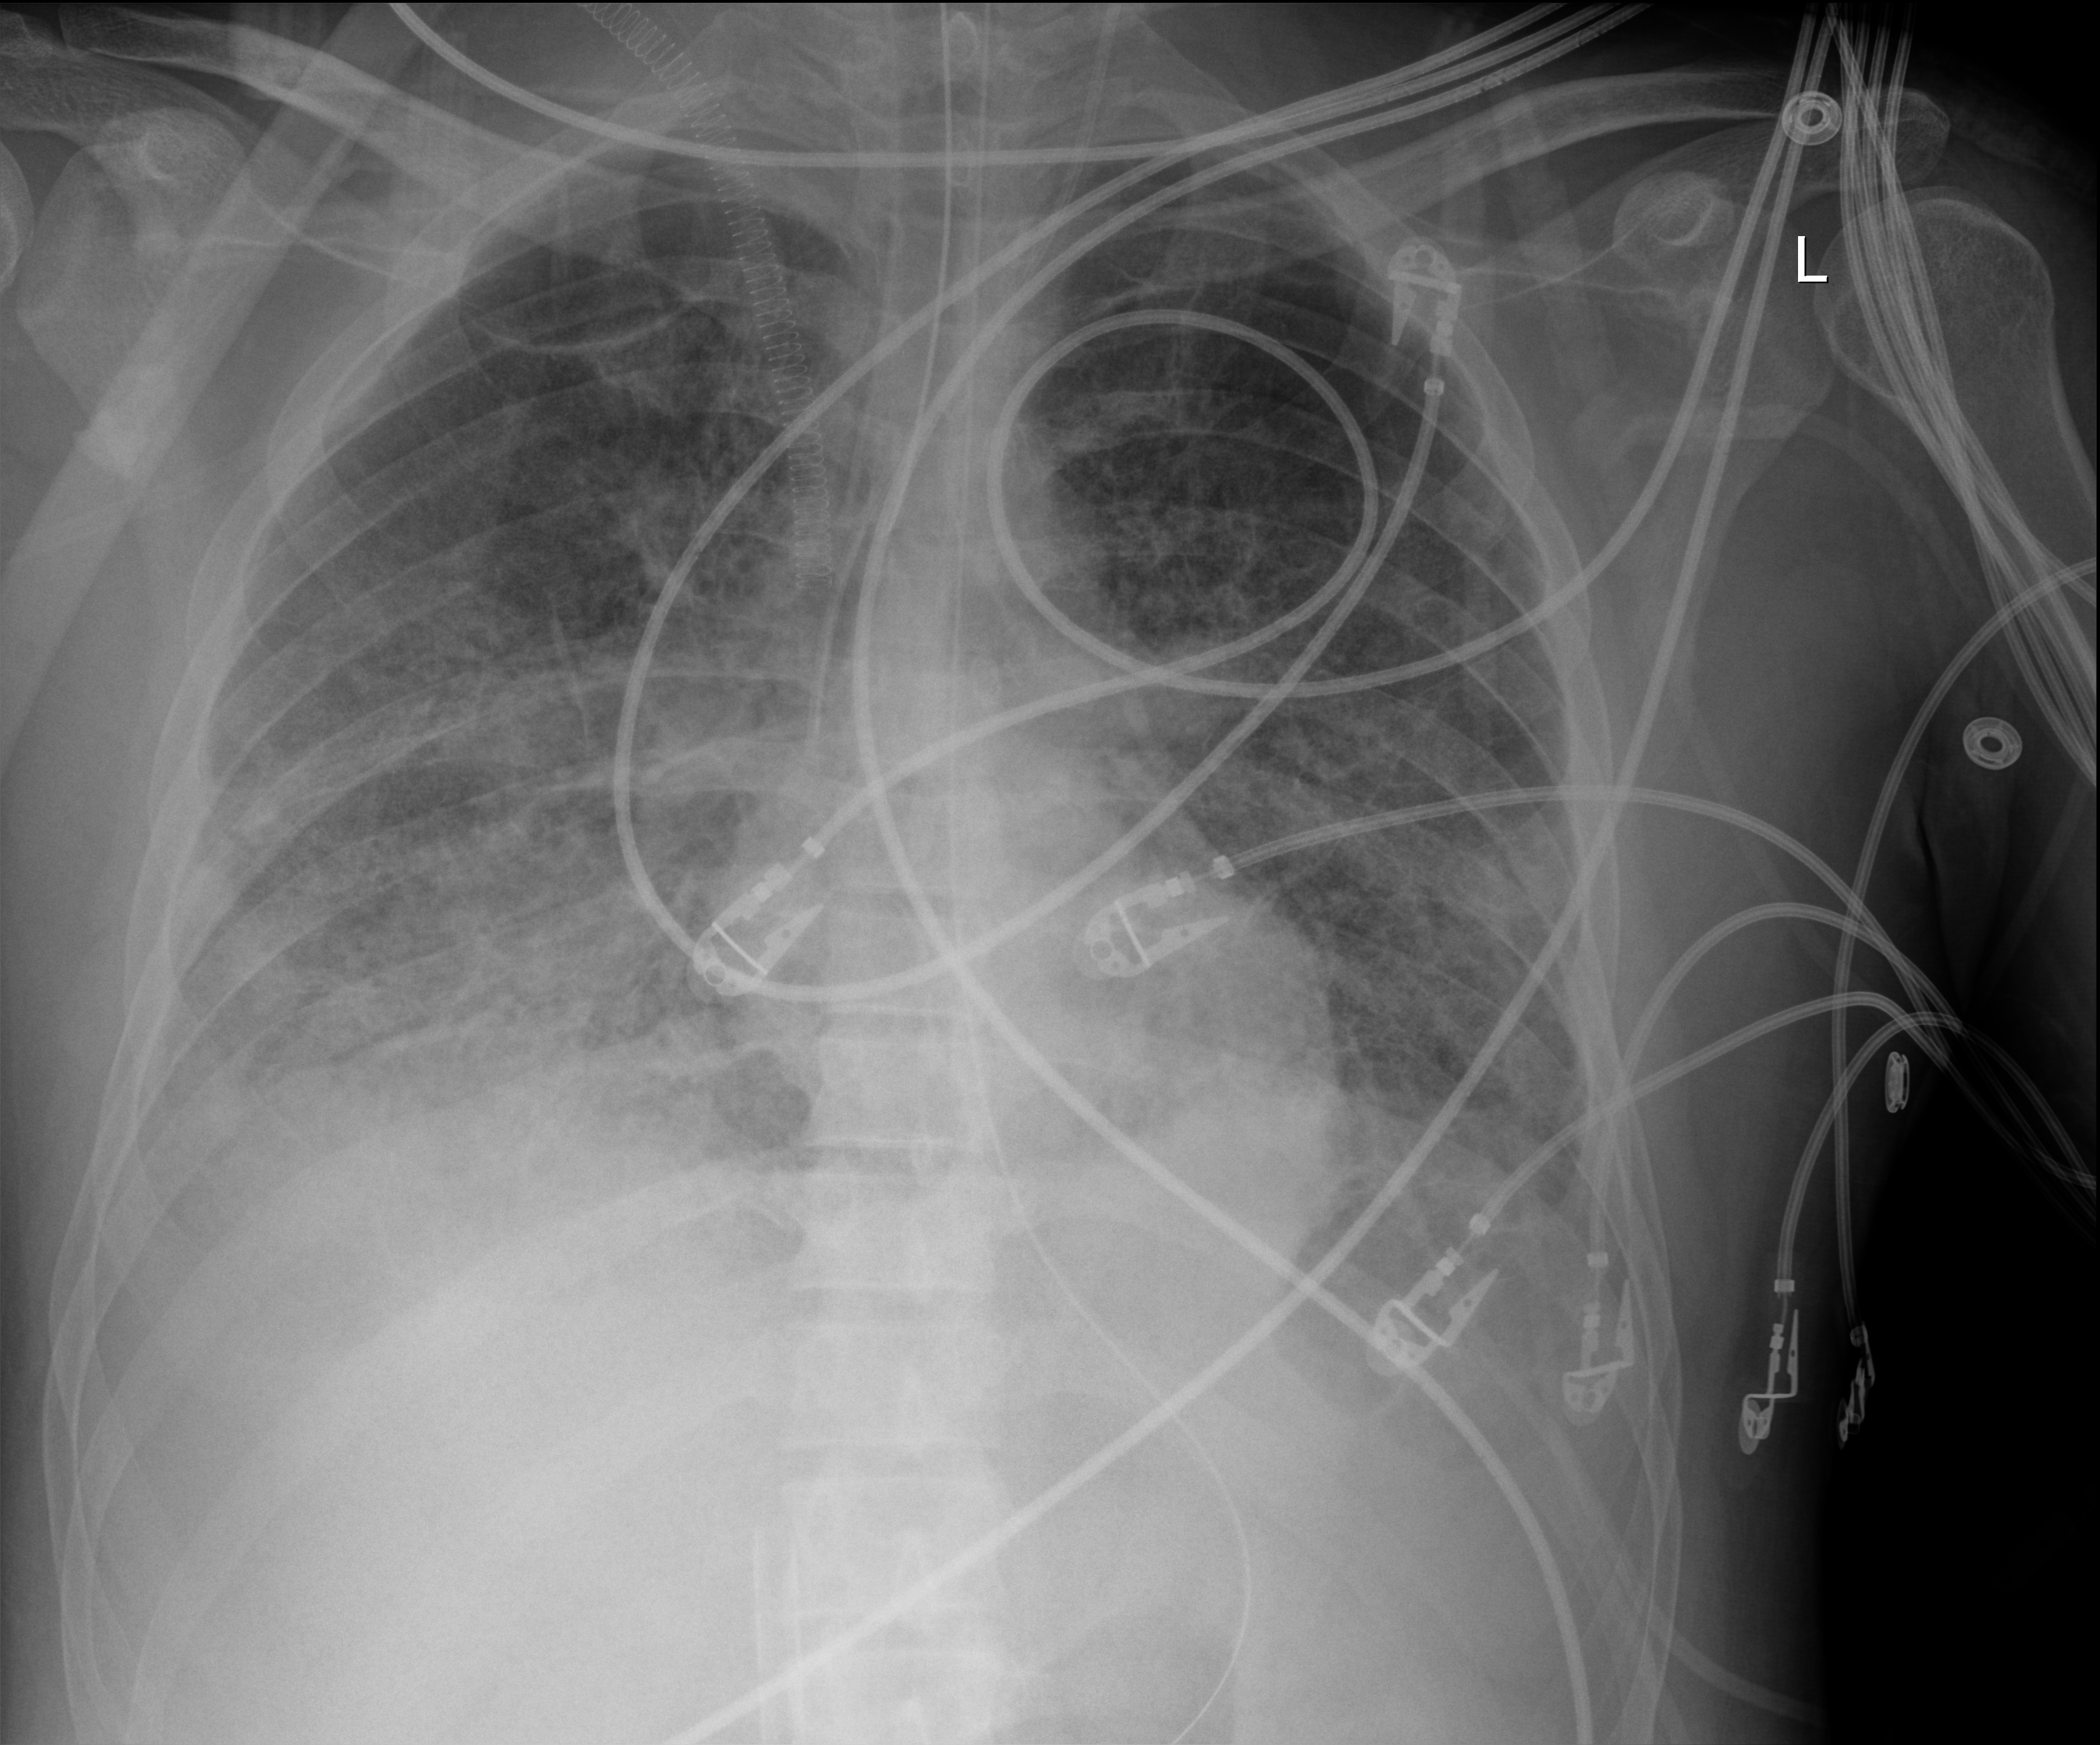
Portable chest radiograph. Patient hospitalised with COVID-19, aged 18–59 years.
Hospital-stay facts (about this admission, not read from this image; timing relative to this image not recorded):
- admitted to intensive care during this hospital stay: yes
- diabetes (admission record): no
- length of hospital stay: 60 days